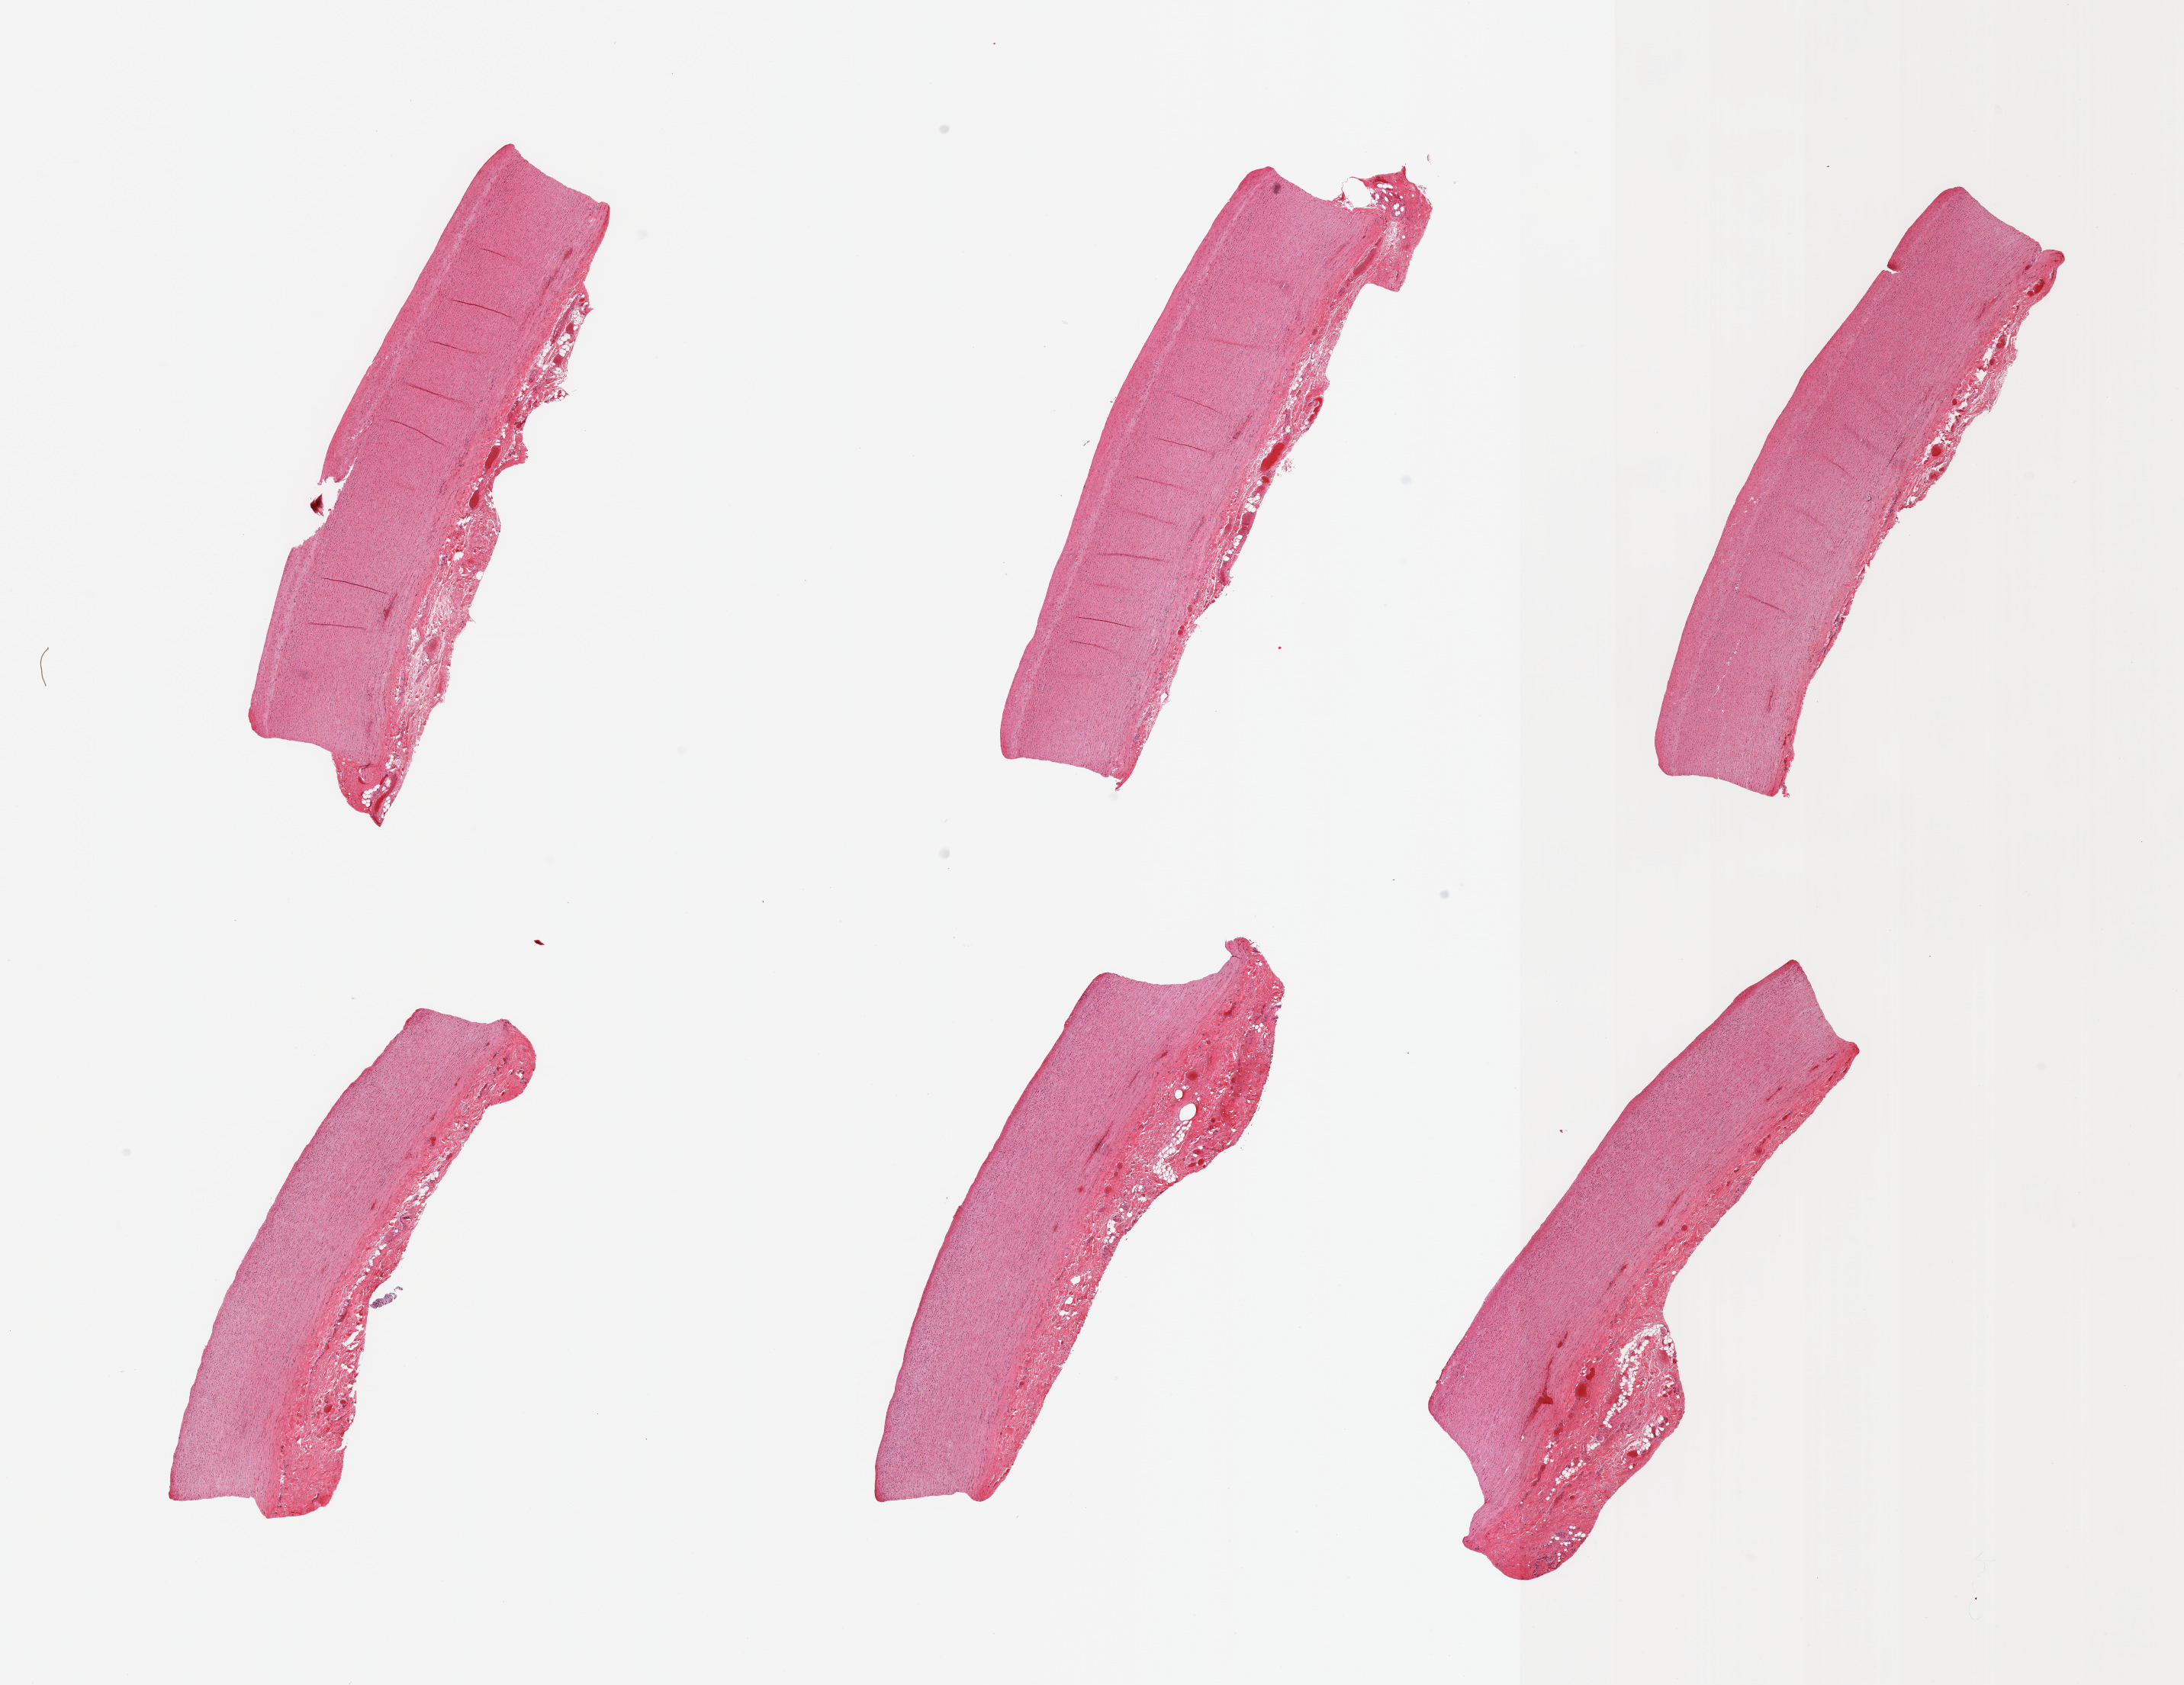
Haematoxylin and eosin whole-slide image, a low-resolution overview of the entire scanned area, about 22.6 x 17.5 mm. PAXgene-fixed, paraffin-embedded tissue. Sampled site (target tissue): aorta. Tissue donor sample. Donor sex: male.
Pathologist's review note for this sample: 6 pieces; some atherosclerosis, up to 1.2mm attached adventitia.